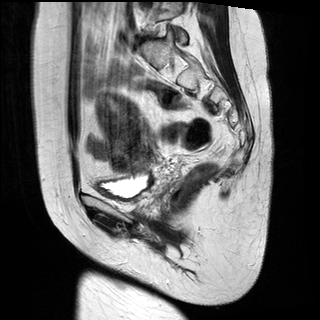
Pelvic MRI for cervical cancer, one sagittal slice; position 17 of 28 along the scan axis; T2-weighted; 1.5 T; TE 89 ms, TR 2740 ms; 320 × 320 image matrix, field of view 260 × 260 mm. Female patient, age 49 years.
Structures marked on this image (expert manual segmentation):
- uterus and cervix: bounding box (x1, y1, x2, y2) in pixels: (95, 91, 154, 175)